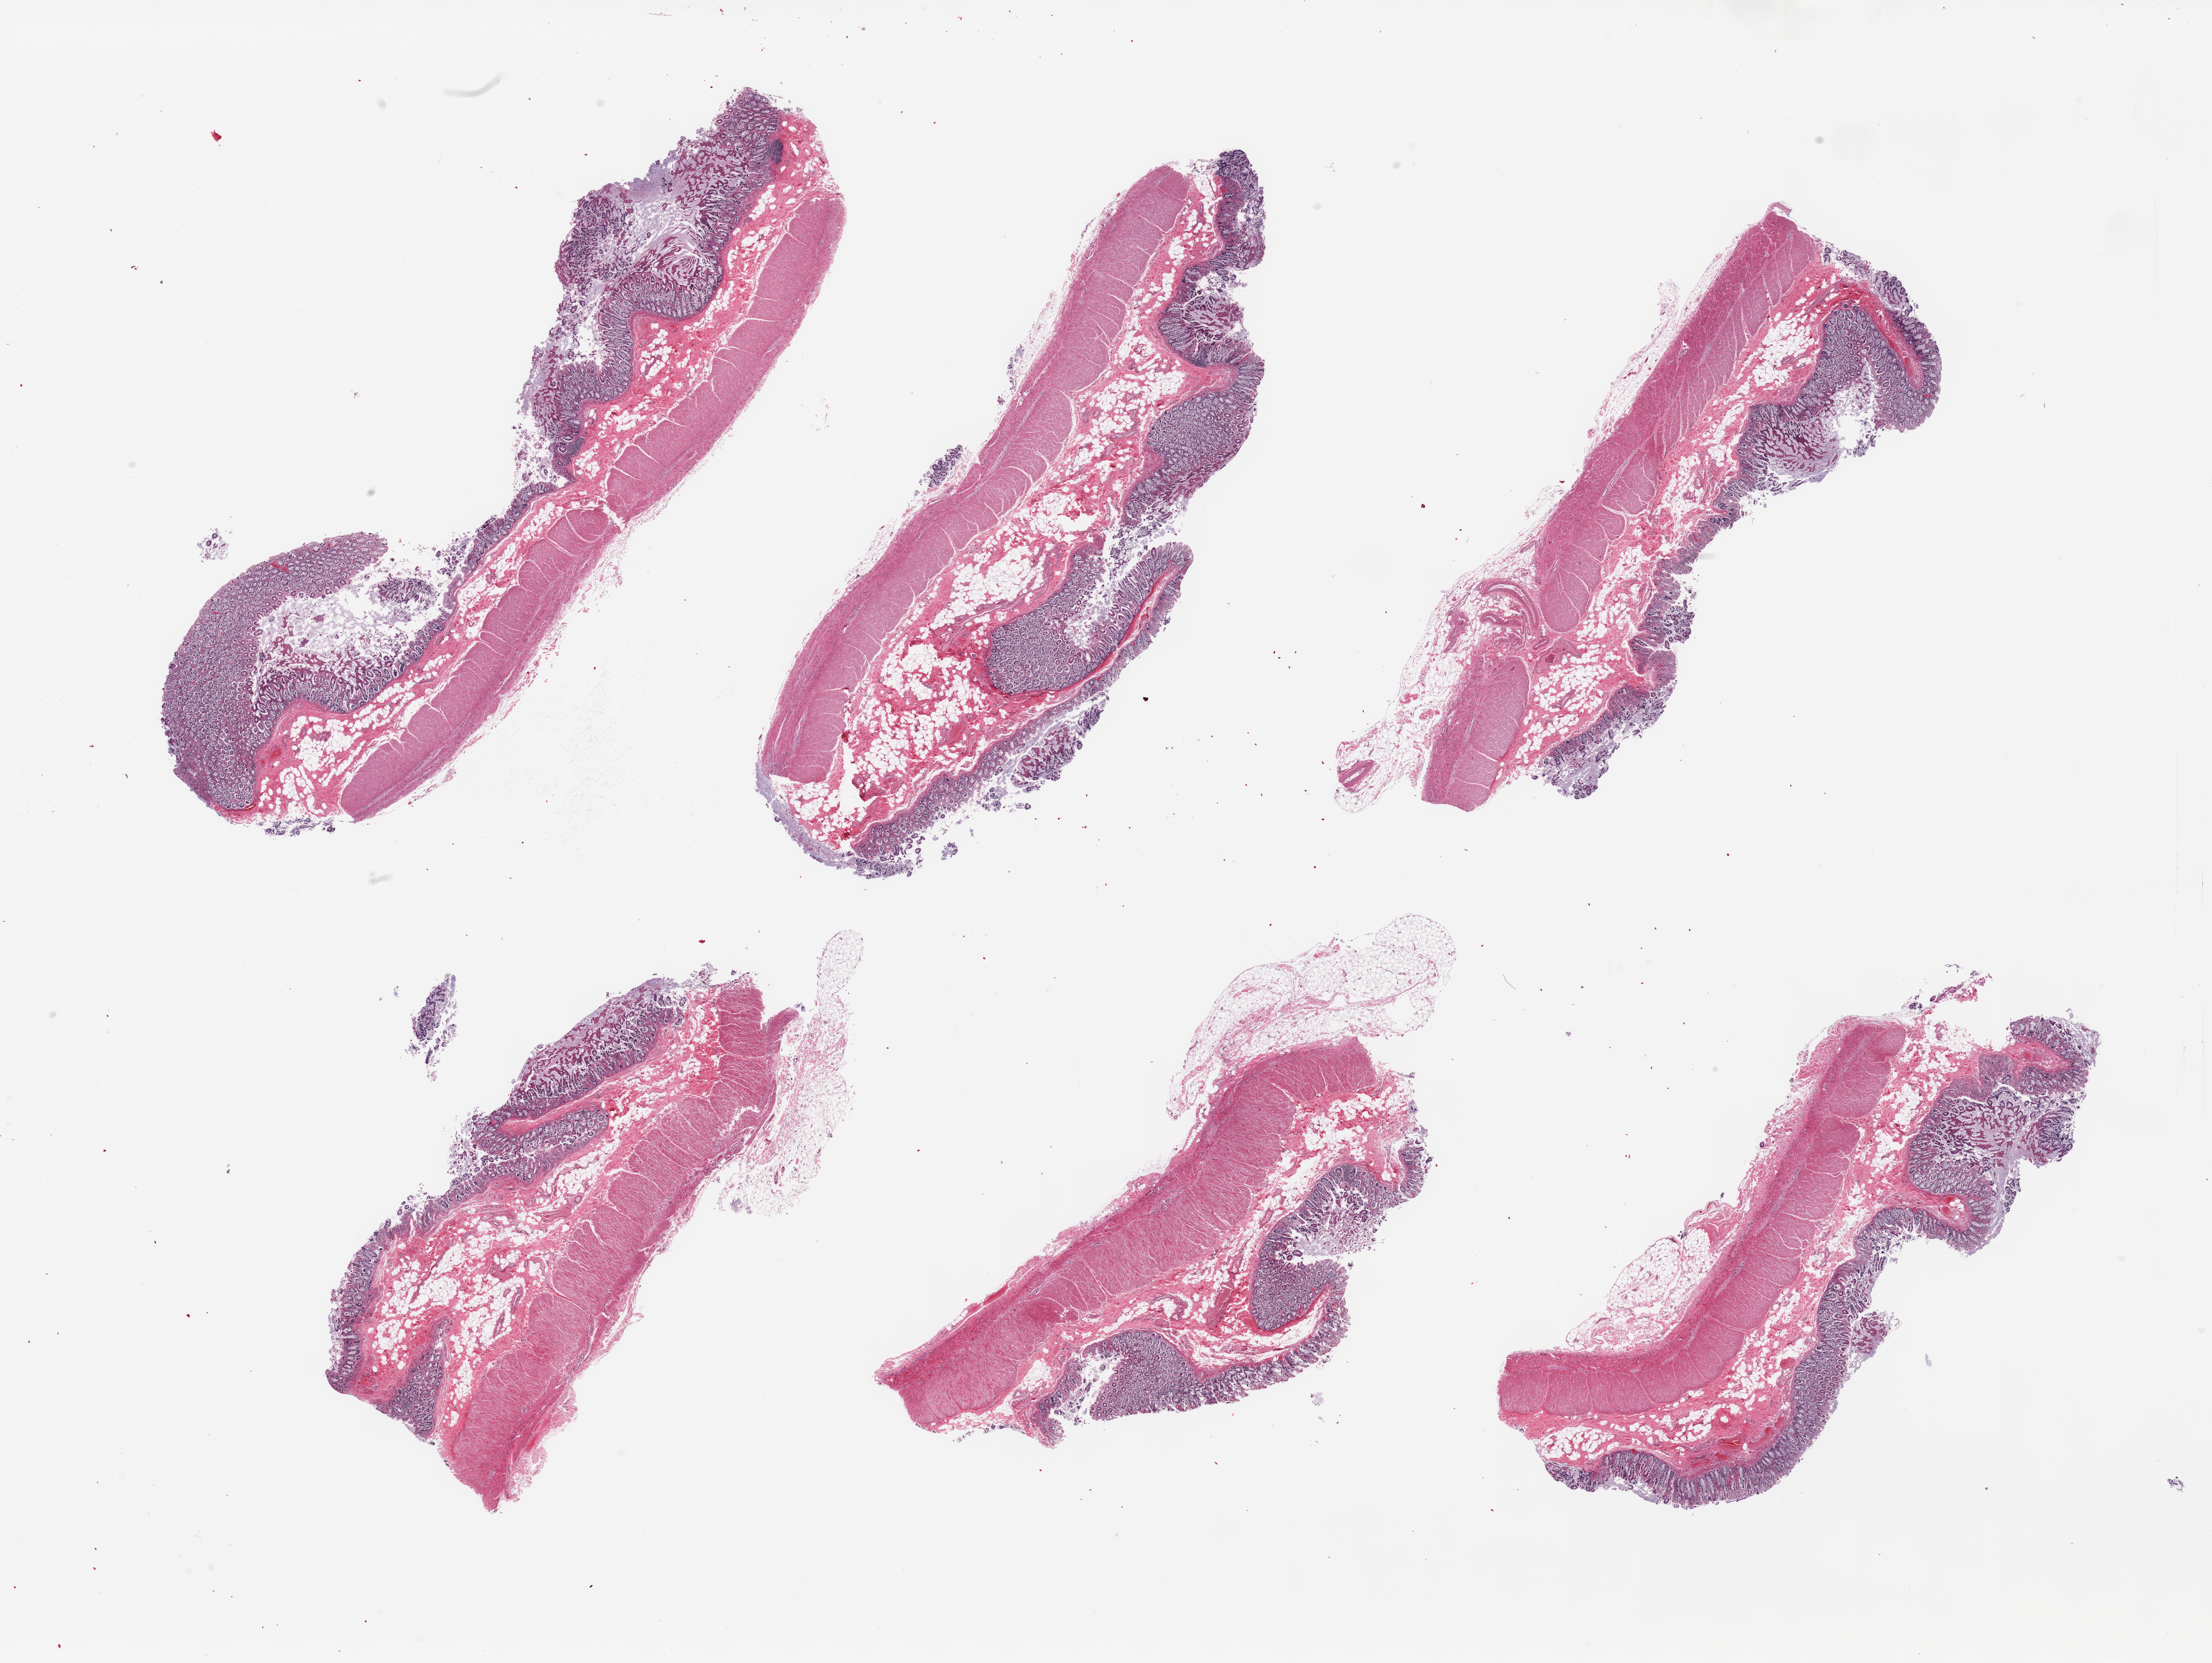
Digitized hematoxylin and eosin (H&E)-stained section, low-resolution overview of the scanned area, about 30.5 x 22.9 mm (acquisition: 20x scan). PAXgene-fixed, paraffin-embedded tissue. Sampled site (target tissue): transverse colon. Donor tissue sample.
Pathologist's review note for this sample: 6 pieces; mucosa up to 1mm but glandular elements completely sloughed.